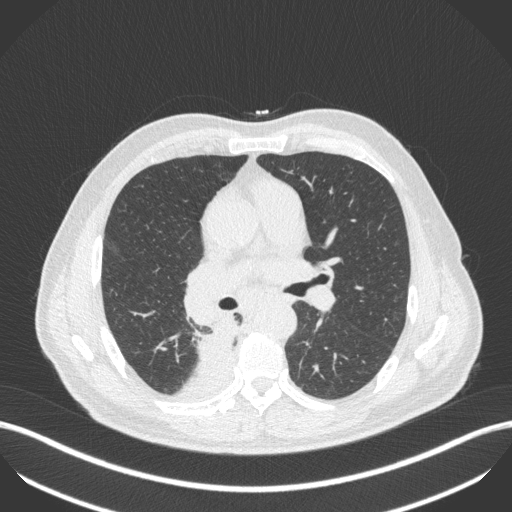
Chest CT, one axial slice. Position 267 of 451 along the scan axis. Reconstruction kernel B31f. Lung window (W 1500 / L -600 HU). 1 mm slice thickness. 512 × 512 image matrix, field of view 400 × 400 mm. Male patient, age 61 years. From the clinical record (not read from this slice): clinical TNM (as recorded): T1 N0 M0.
Annotated regions visible in this slice (rectangle marked by the reading radiologist):
- lung tumour (recorded histology: small cell carcinoma): bounding box <196,318,239,368> (left, top, right, bottom; pixels)